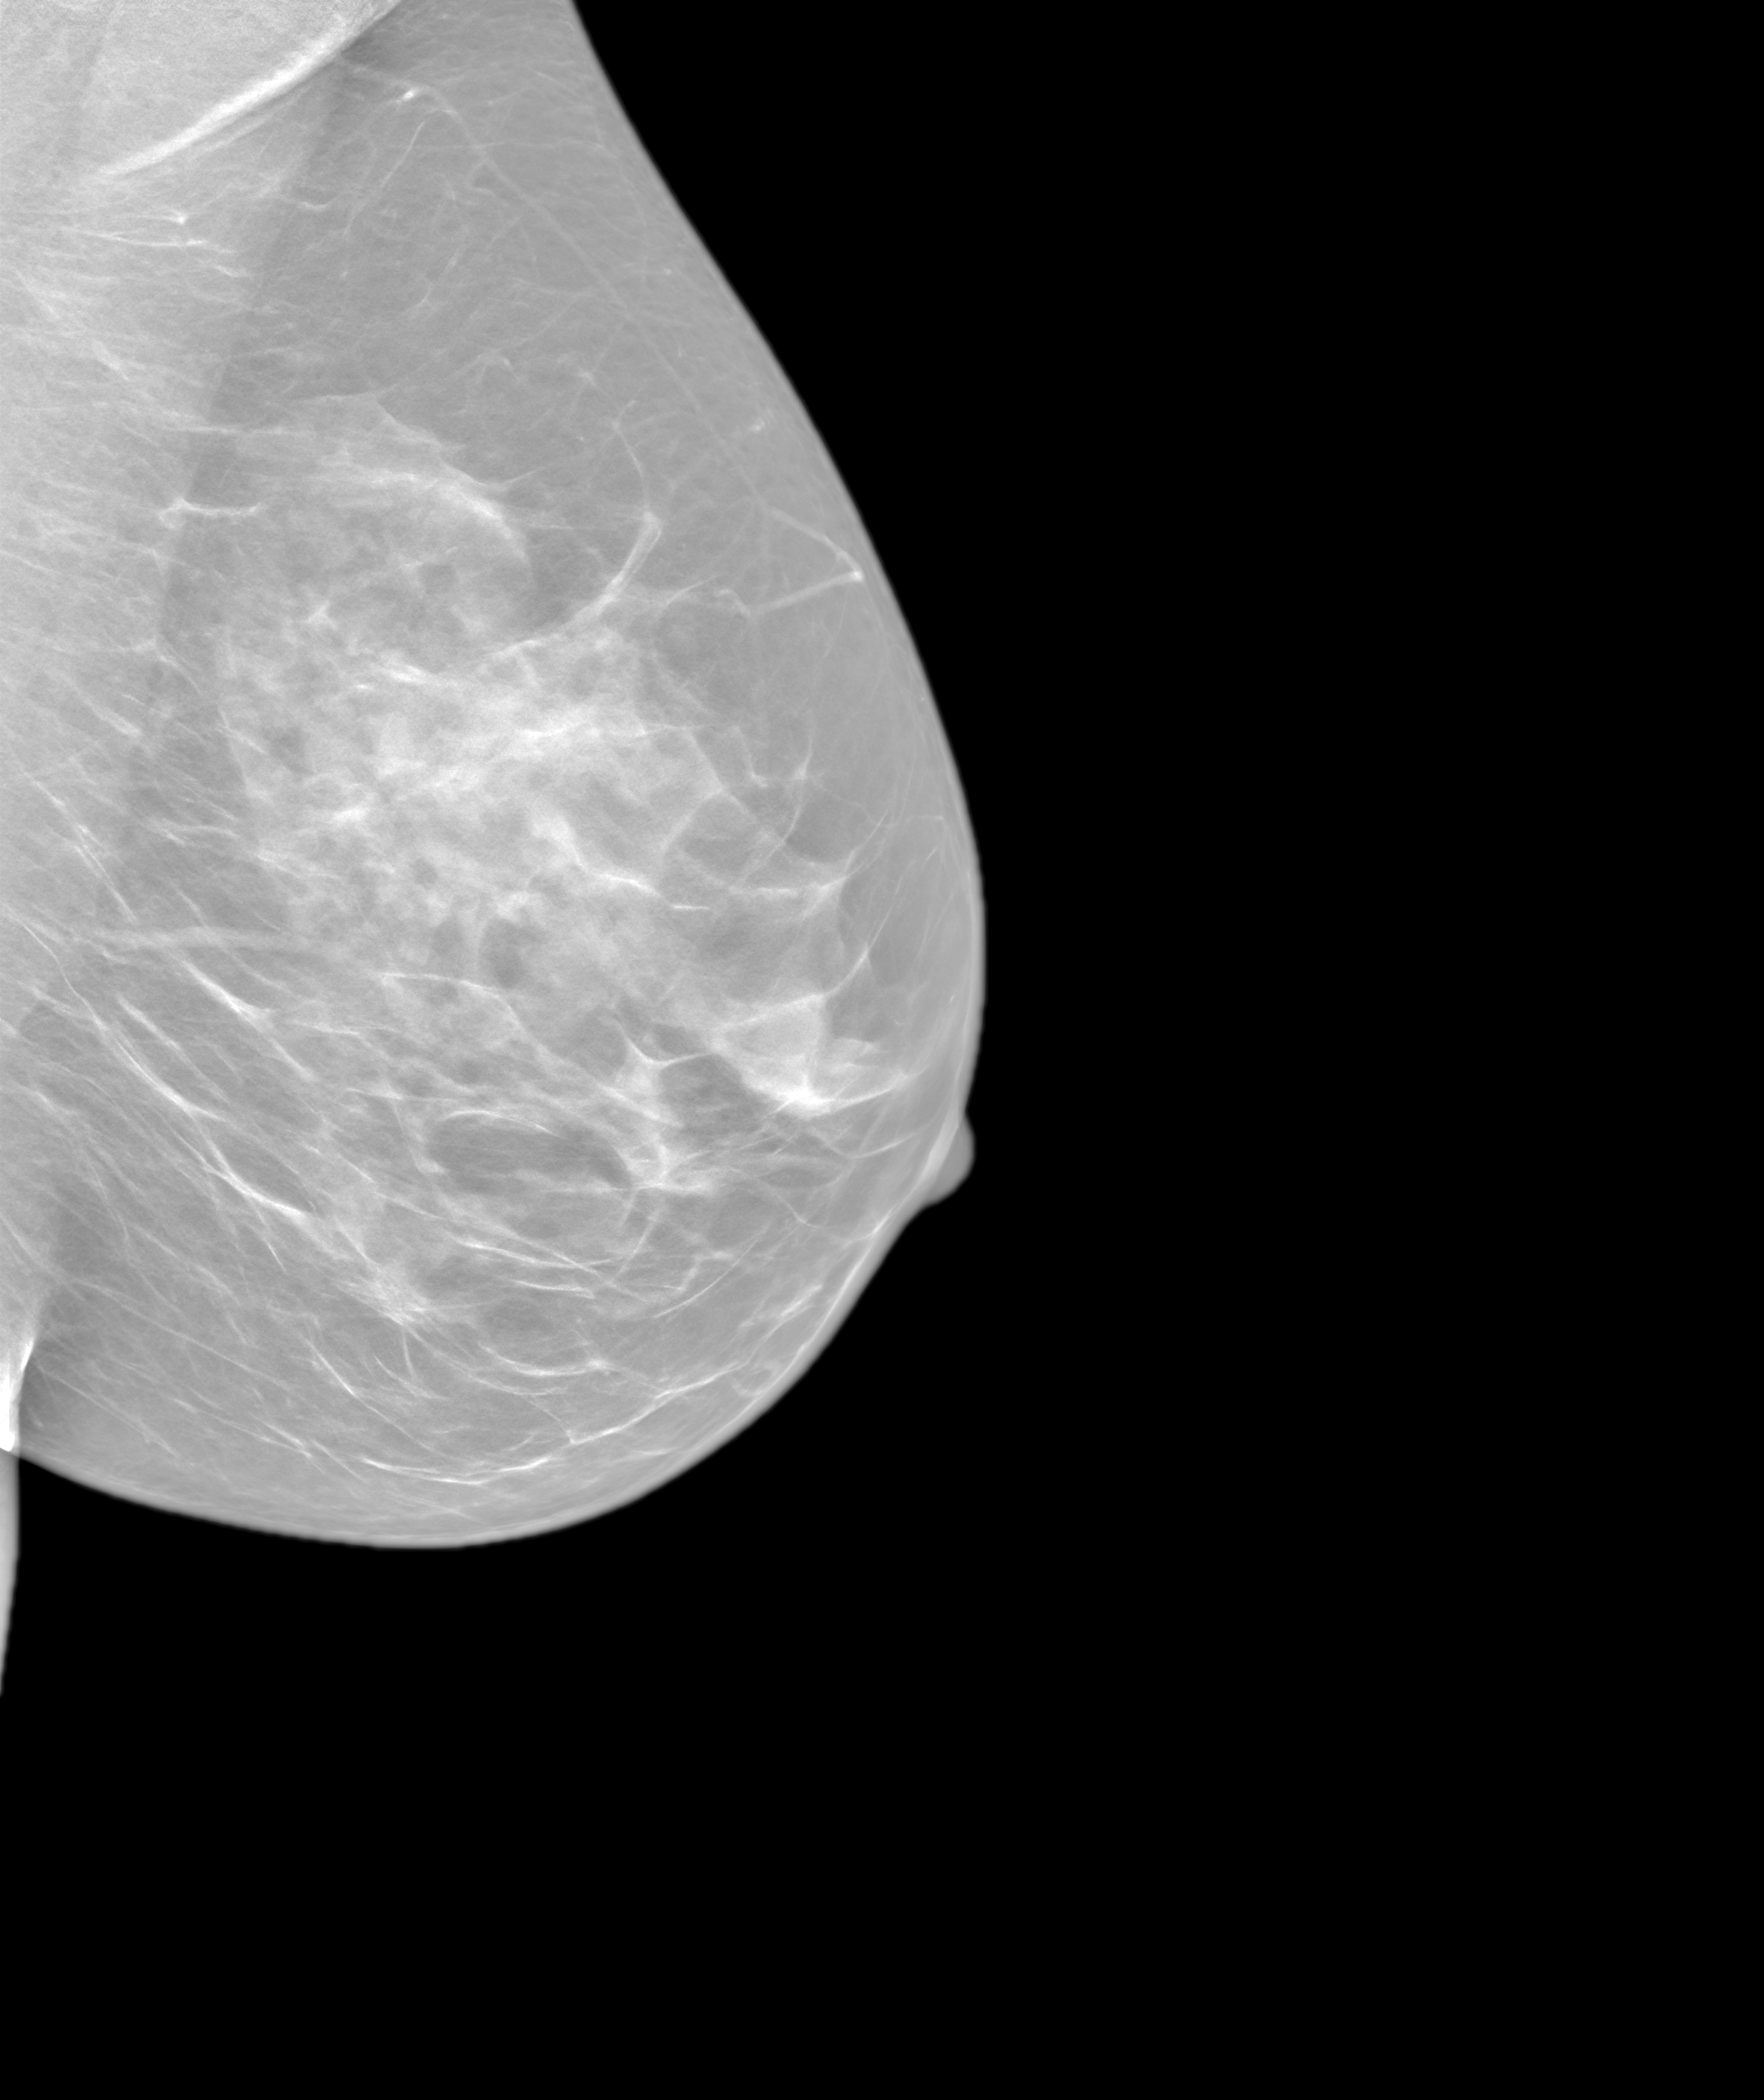
Synthesized 2-D mammogram reconstructed from digital breast tomosynthesis, left breast, MLO view, annual screening mammography examination, system: SenoIris_1SP1.1(421). Patient aged 56 years (female).
BI-RADS breast density category at the screening exam (both breasts, scale 1–4): 3. Final BI-RADS assessment for this screening round (tomosynthesis exam, both breasts): category 1. Recall: no recall after this screen.